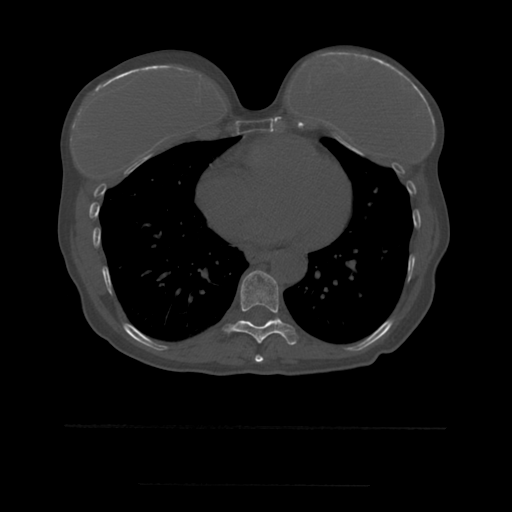
CT including the spine, one axial slice; position 320 of 544 along the scan axis; bone window (W 1800 / L 400 HU); 512 × 512 image matrix, field of view 350 × 350 mm. Patient age 58 years. From the clinical record (not read from this slice): primary cancer: lung.
Structures marked on this image (semi-automatic segmentation, software-assisted and operator-edited):
- T8 vertebra: bounding box <255,355,264,363> (left, top, right, bottom; pixels)
- T9 vertebra: <224,271,297,345>